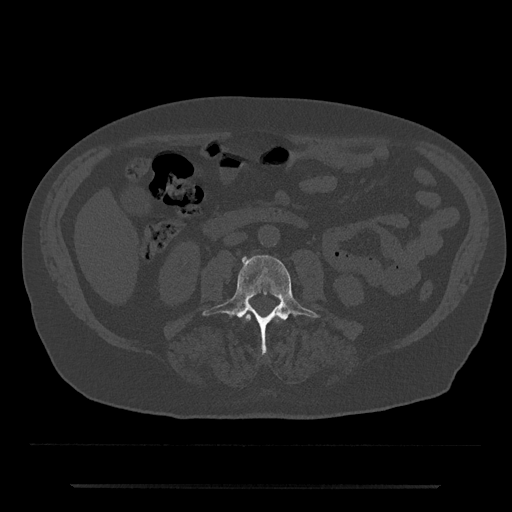
CT including the spine, one axial slice; position 415 of 797 along the scan axis; 120 kVp; bone window (W 1800 / L 400 HU); 0.5 mm slice thickness; 512 × 512 image matrix, field of view 434 × 434 mm. Male patient, age 80 years. From the clinical record (not read from this slice): primary cancer: prostate; vertebrae with lytic lesions (as recorded): L1, T11.
Annotated regions visible in this slice (semi-automatically segmented with operator editing):
- L2 vertebra: bounding box [x1, y1, x2, y2] px = [246, 315, 279, 321]
- L3 vertebra: [202, 255, 320, 355]